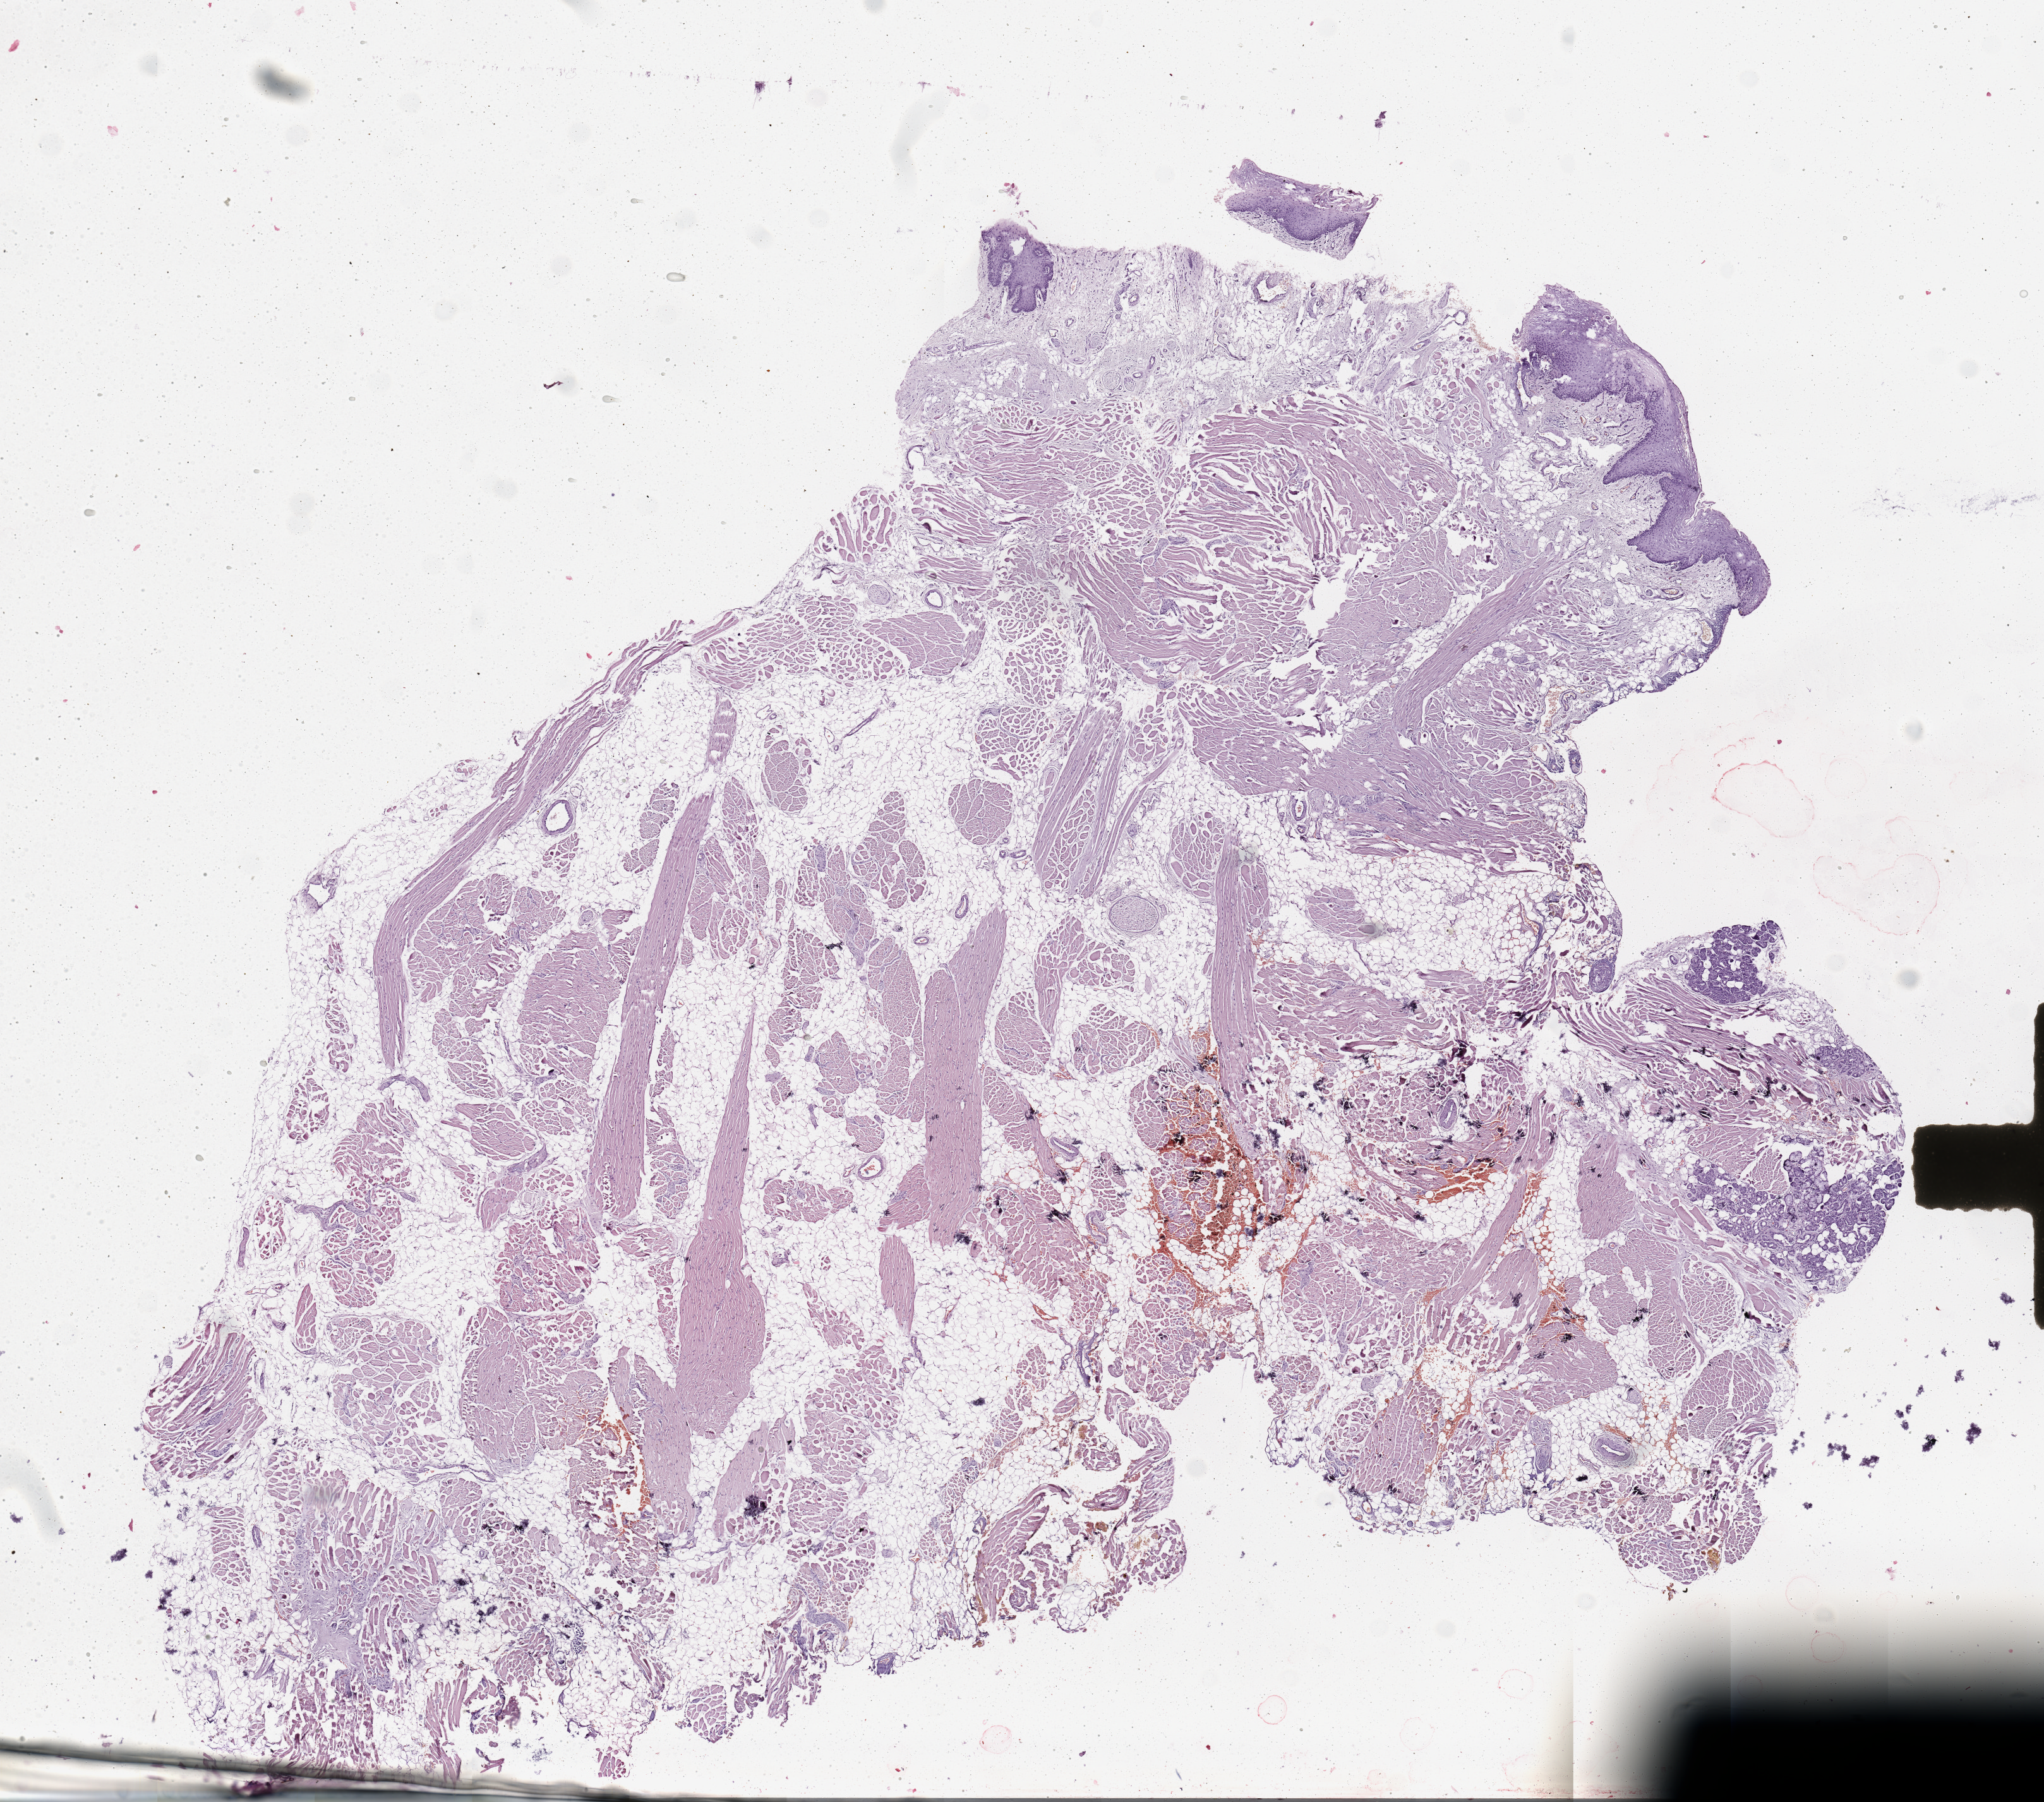
Whole-slide histology image, Hematoxylin and eosin (H&E) stained — a low-resolution overview of the entire scanned area, about 12.8 x 11.3 mm; normal (non-tumour) tissue sample, sampled site: tongue. 61-year-old male patient.
This section: normal (non-tumour) tissue from the same patient. Patient diagnosis: Squamous cell carcinoma, NOS (tongue, NOS).